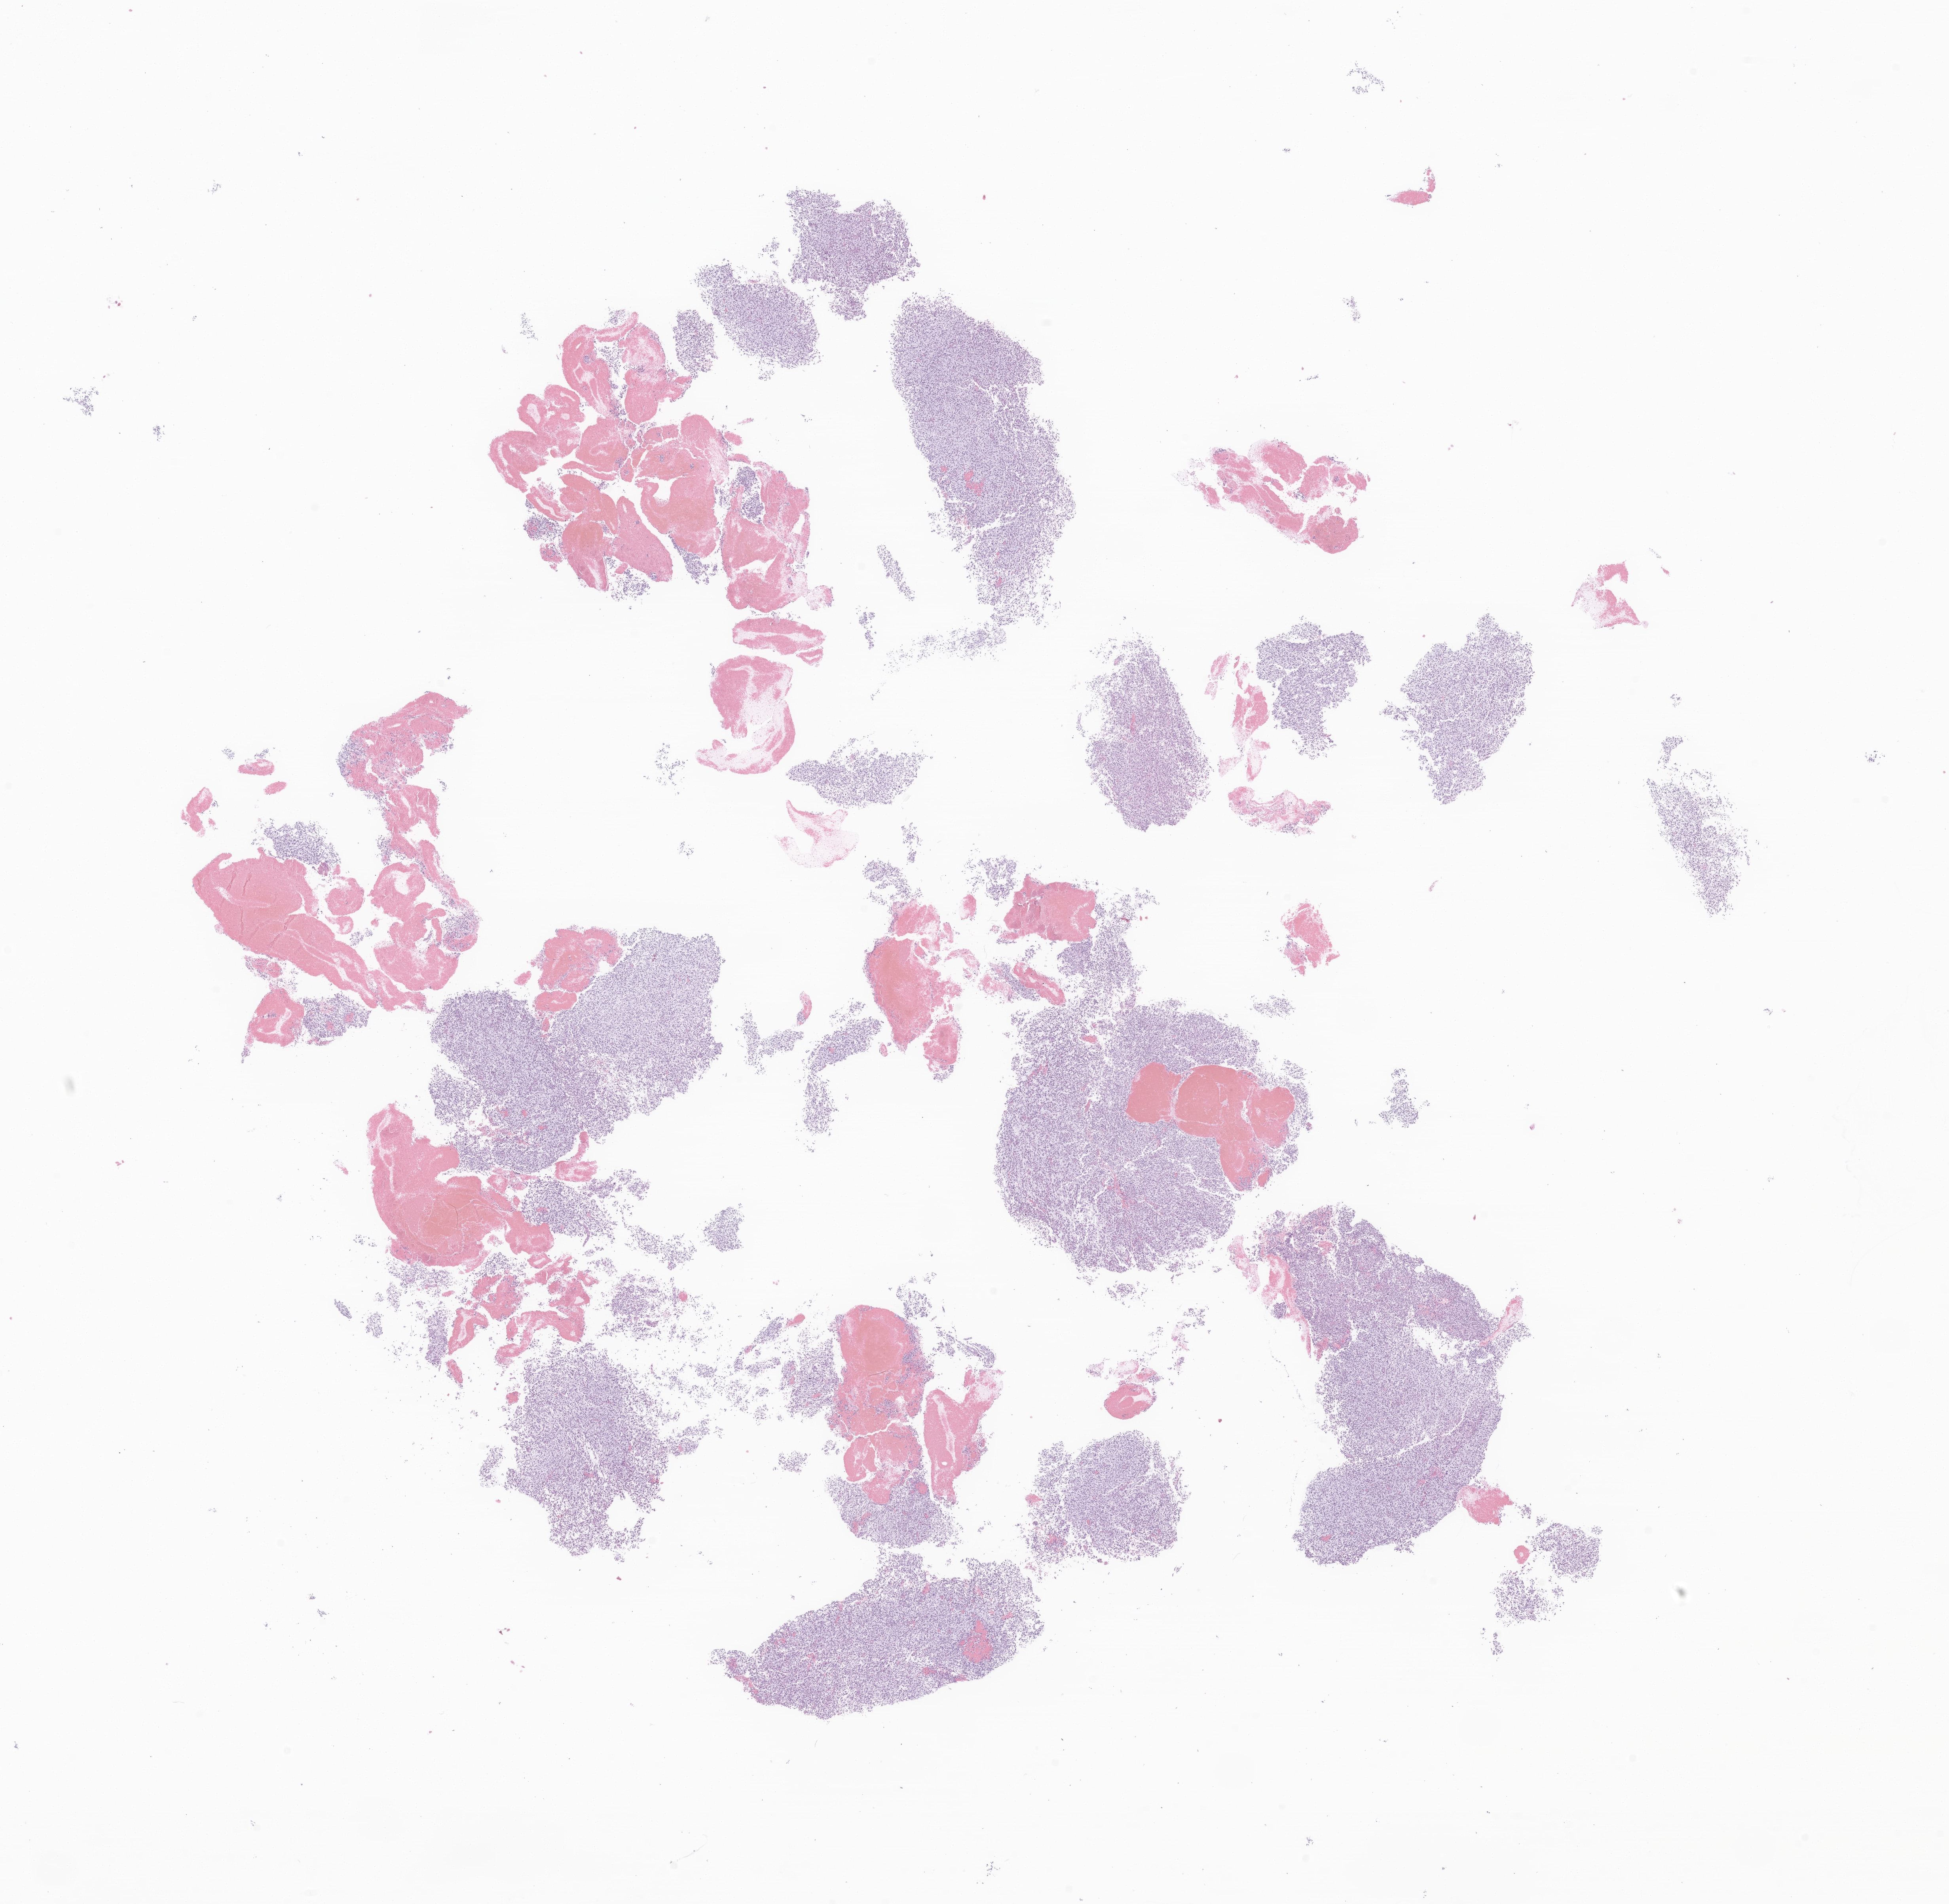
Hematoxylin and eosin (H&E) whole-slide image of tumor tissue from the brain, whole scanned area (about 20.8 x 20.3 mm) shown as a low-resolution overview, formalin-fixed paraffin-embedded section. Patient male; age 201 months (16 years 9 months).
Recorded diagnosis: Ganglioneuroma.